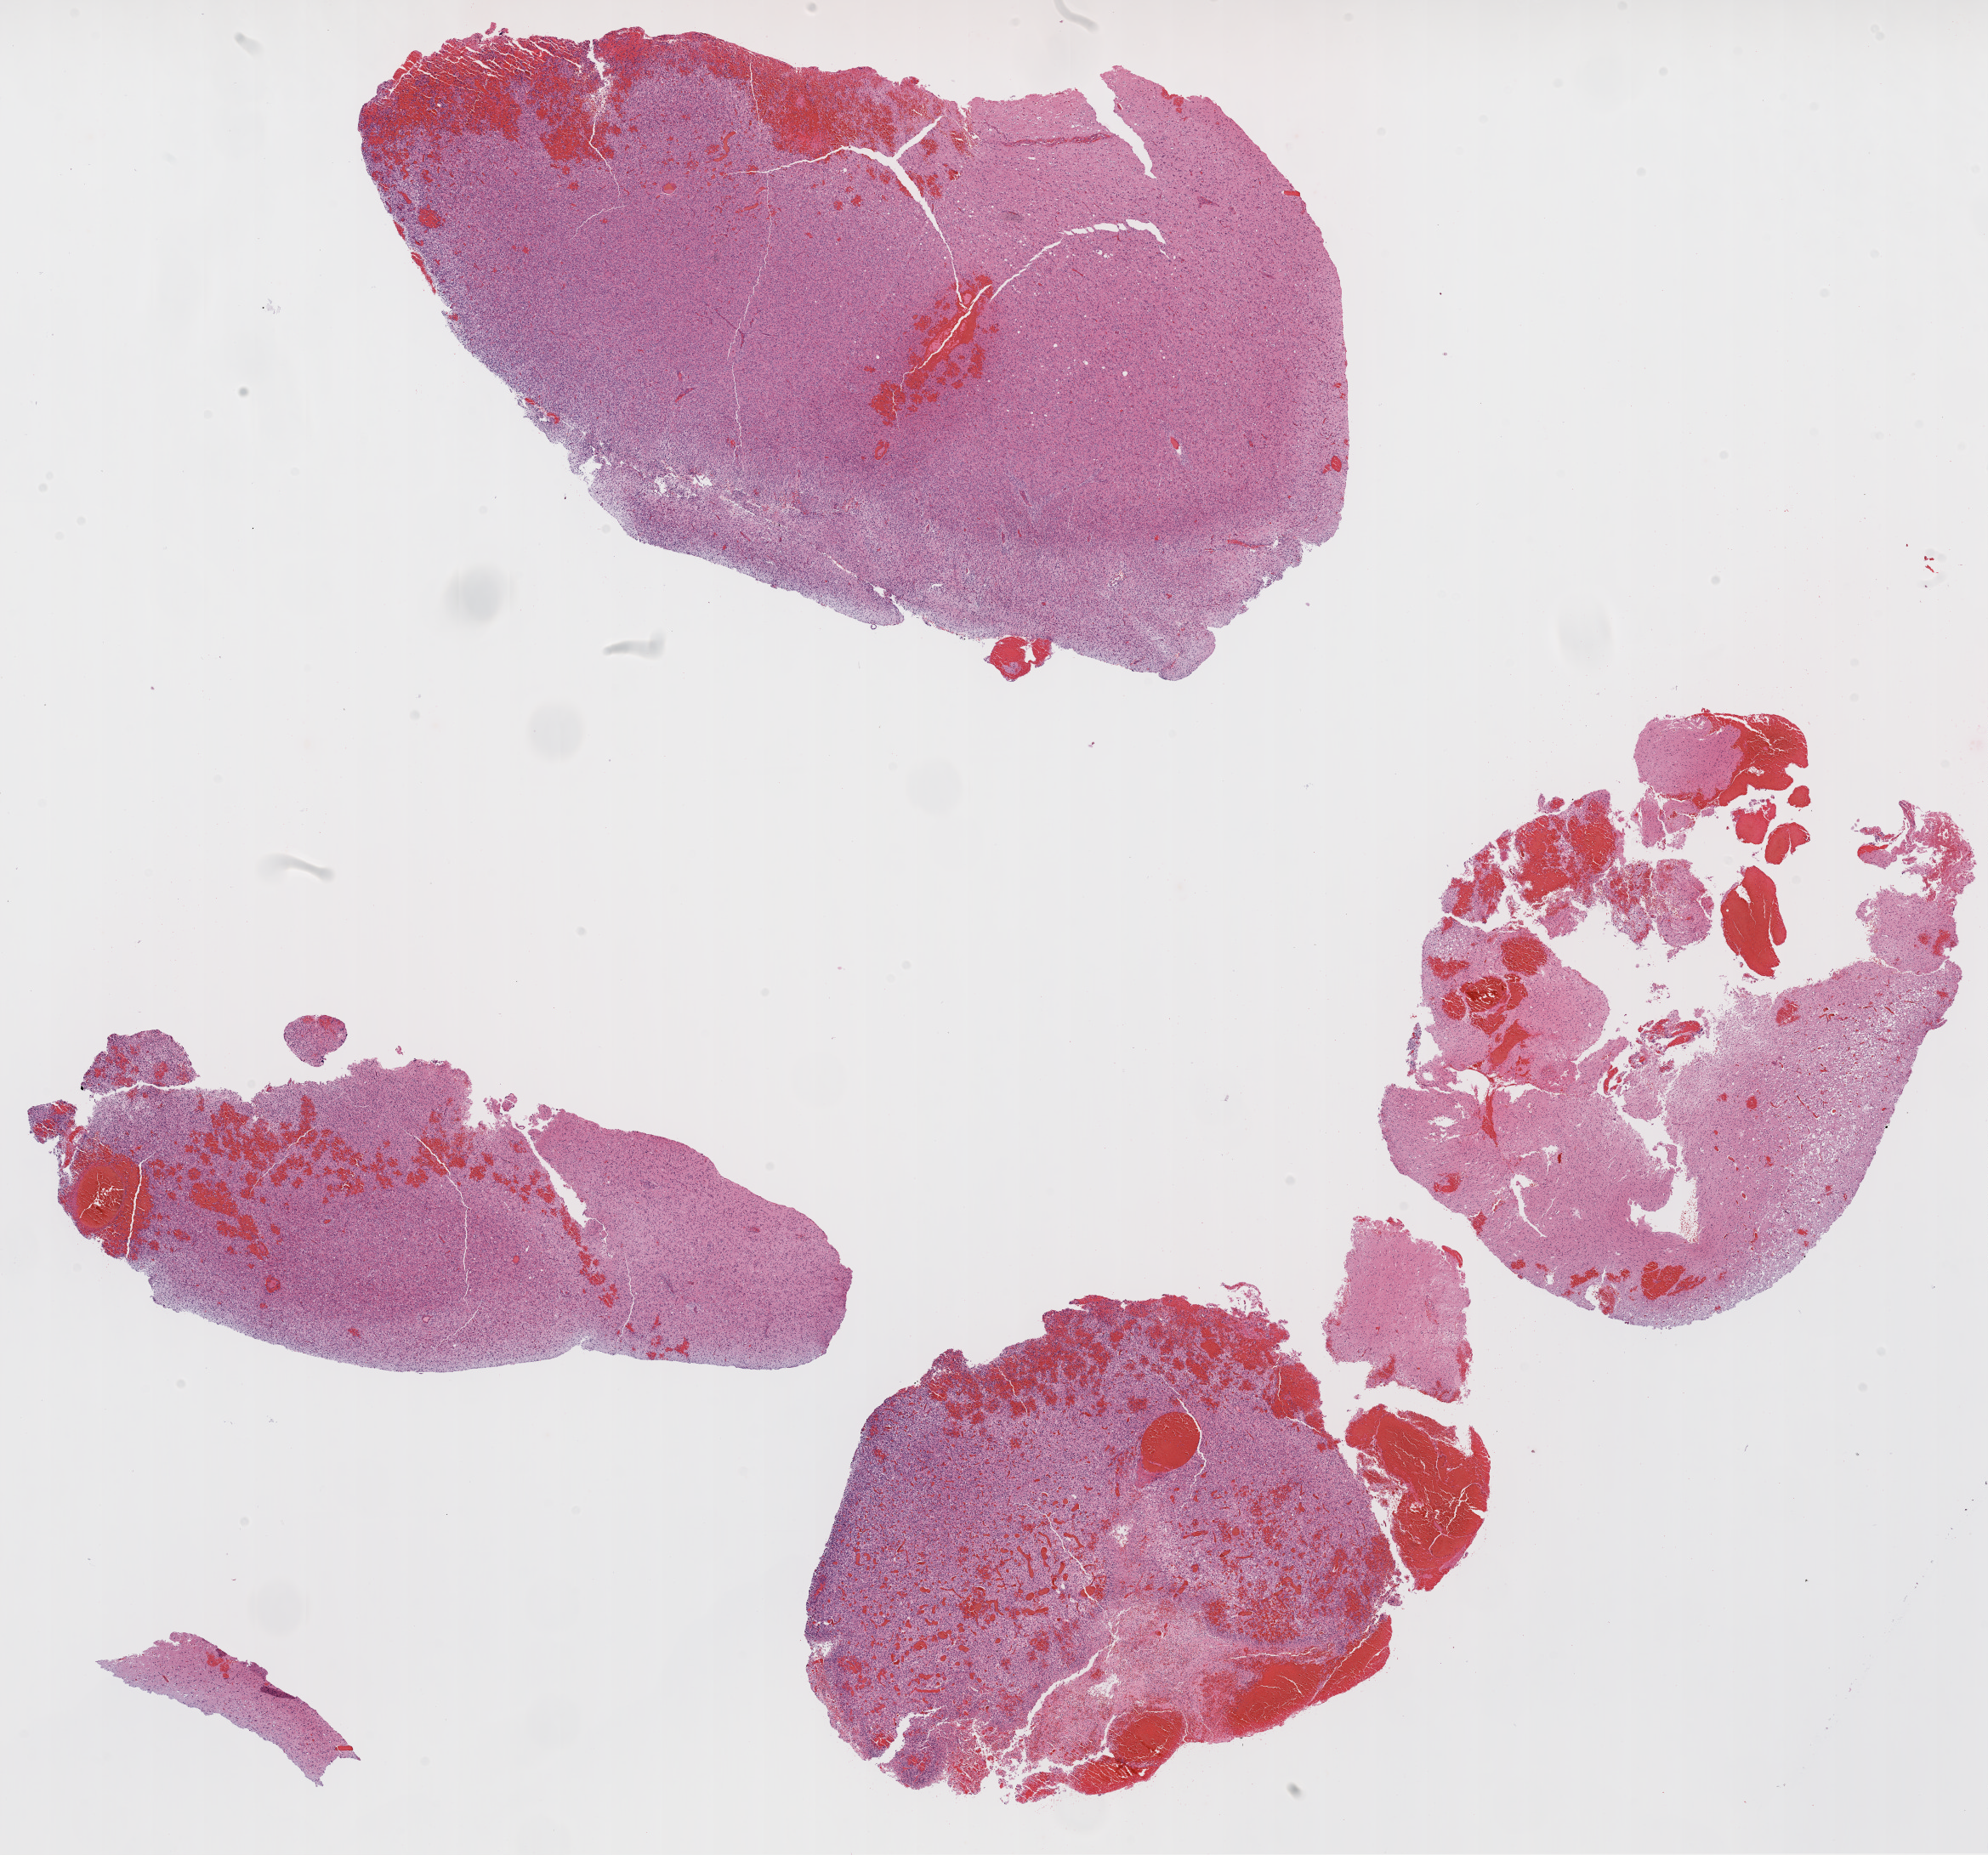
Digitized H&E tissue section (whole slide) — whole scanned area (about 18.9 x 17.6 mm, acquisition: 20x scan) shown as a low-resolution overview; formalin-fixed paraffin-embedded (FFPE) diagnostic section; sample: primary tumour, brain. Male, age 54 years at initial diagnosis.
• histologic diagnosis: Glioblastoma